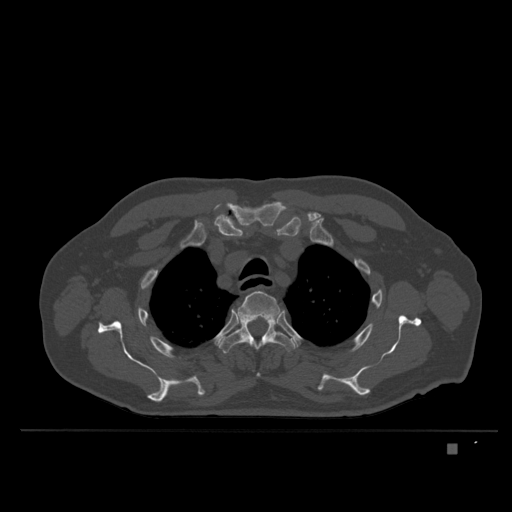
CT including the spine, one axial slice; position 293 of 435 along the scan axis; bone window (W 1800 / L 400 HU); 1.5 mm slice thickness; 512 × 512 image matrix, field of view 434 × 434 mm. Patient: male, 73 years. Case-level facts recorded for this patient, not image findings: primary cancer: skin.
Annotated regions visible in this slice (semi-automatic segmentation, software-assisted and operator-edited):
- T3 vertebra: bounding box <237,291,281,377> (left, top, right, bottom; pixels)
- T4 vertebra: <218,318,296,354>